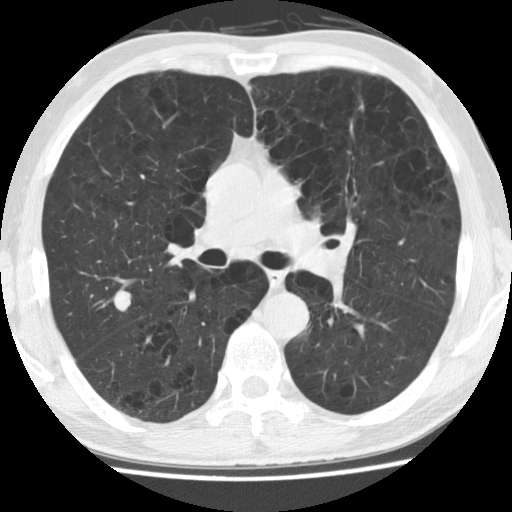
Low-dose screening chest CT, one axial slice; slice 90 of 158 in the series (ordered by position); reconstruction kernel STANDARD; lung window (W 1500 / L -600 HU); 512 × 512 image matrix, field of view 324 × 324 mm.
Outlined on this slice (expert manual segmentation):
- lesion 1 (tumor, upper lobe of right lung): box from (x=113, y=291) to (x=131, y=311) px